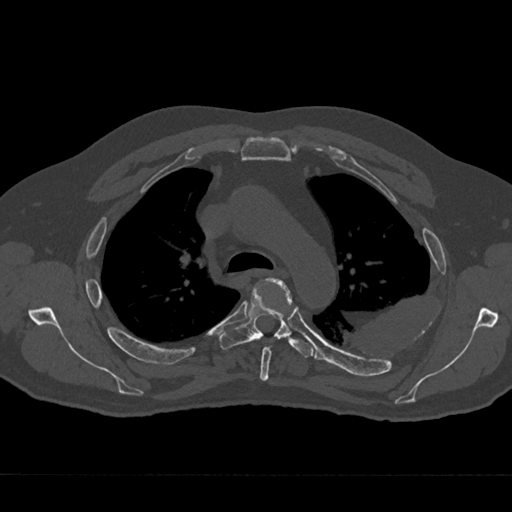
CT including the spine, one axial slice. Slice 493 of 797 in the series (ordered by position). 120 kVp. Bone window (W 1800 / L 400 HU). 512 × 512 image matrix. Male patient, age 75 years. From the clinical record (not read from this slice): primary cancer: renal; vertebrae with lytic lesions (as recorded): T4.
Annotated regions visible in this slice (semi-automatically segmented with operator editing):
- T4 vertebra: bounding box [x1, y1, x2, y2] px = [260, 278, 292, 381]
- T5 vertebra: [219, 278, 314, 357]